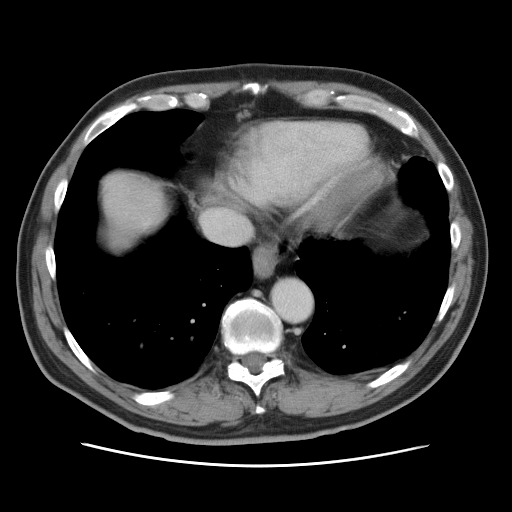
Contrast-enhanced abdominal CT, one axial slice. Intravenous contrast given. Soft-tissue window (W 400 / L 40 HU). 5 mm slice thickness. 512 × 512 image matrix, field of view 370 × 370 mm. Male patient, age 69 years. From the clinical record (not read from this slice): diagnosis: colorectal cancer liver metastases, imaged before liver resection; multiple liver metastases: no.
Outlined on this slice (manually delineated by an expert):
- hepatic veins: box from (x=202, y=210) to (x=250, y=244) px
- liver: (x=102, y=174)–(x=165, y=242)
- planned liver remnant (the part of the liver to remain after resection): (x=113, y=217)–(x=149, y=235)